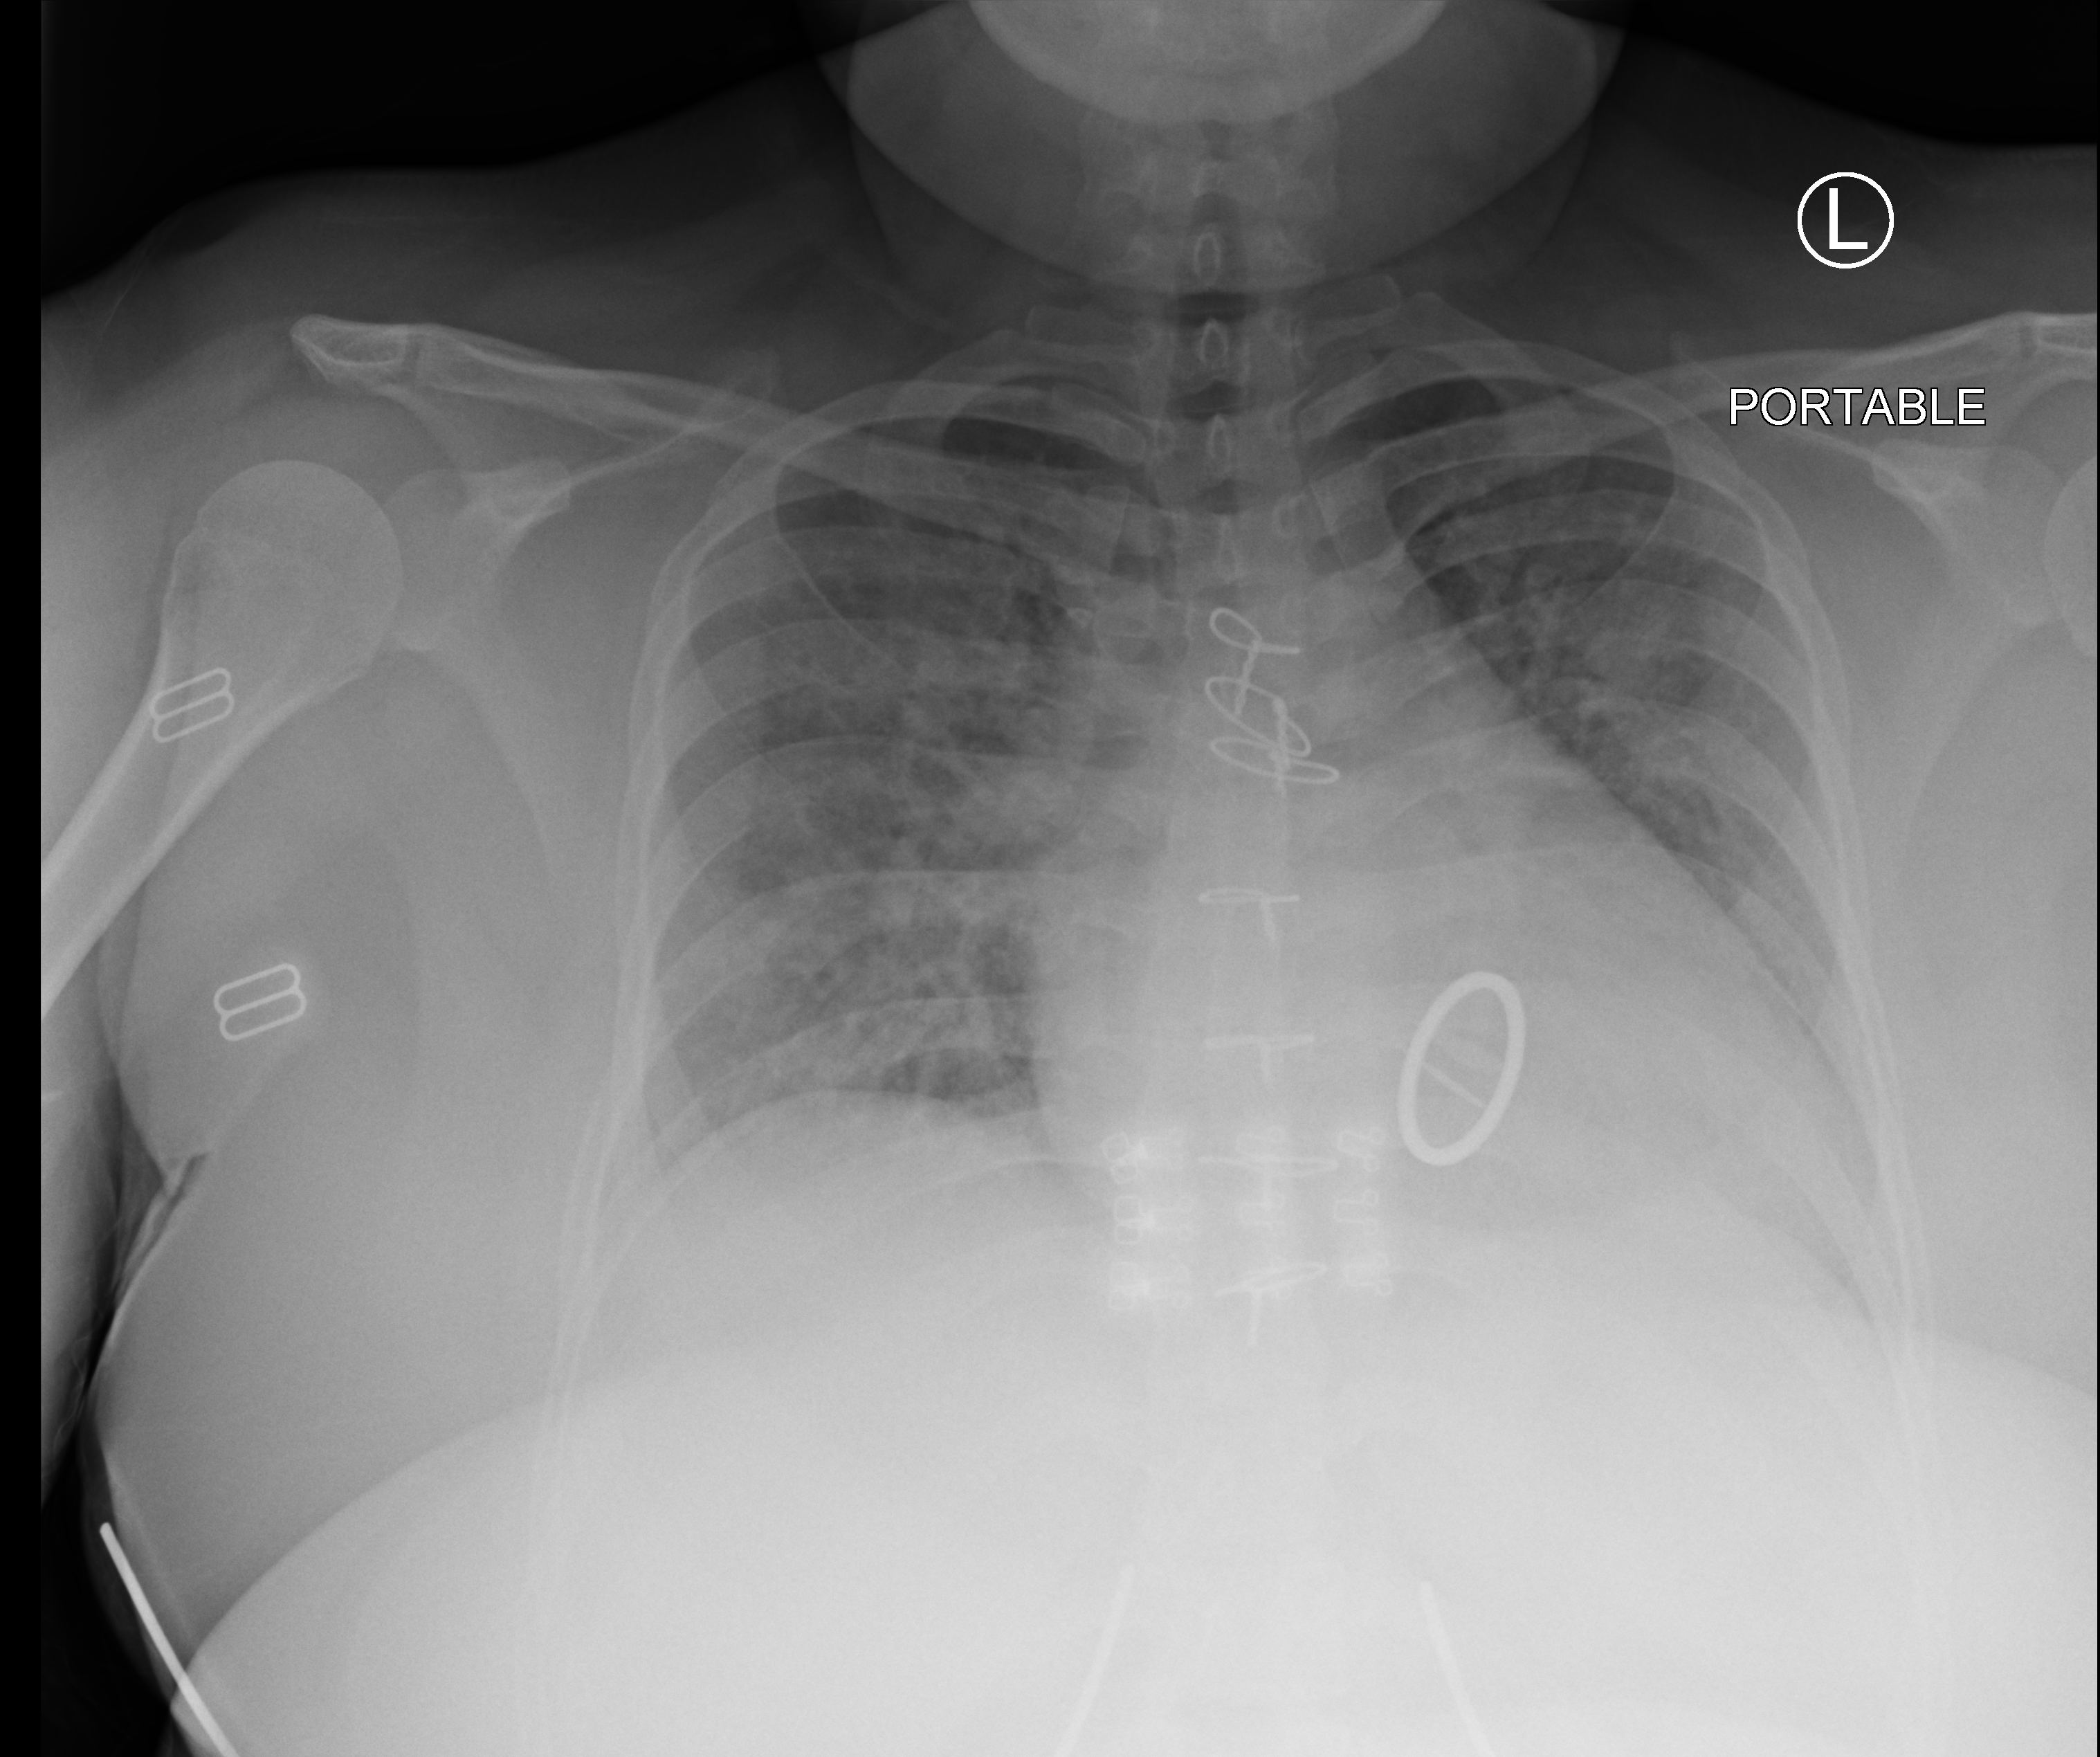
Portable chest radiograph; anteroposterior (AP) projection. Patient hospitalised with COVID-19; female, aged 18–59 years.
Hospital-stay facts (about this admission, not read from this image; timing relative to this image not recorded): length of hospital stay: 3 days; admitted to intensive care during this hospital stay: no; mechanically ventilated during this hospital stay: no.